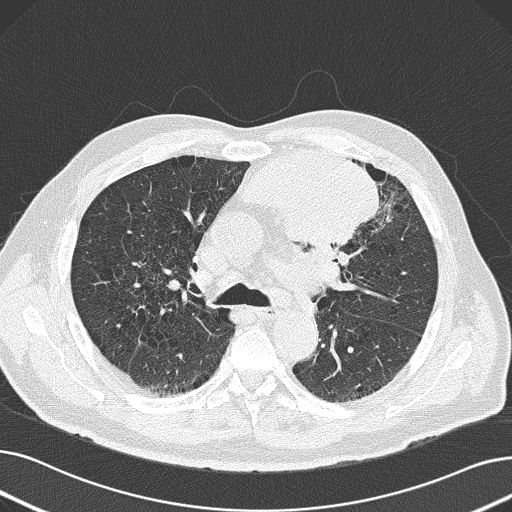
Axial slice from a low-dose chest CT screening exam; baseline annual screen; lung window (W 1500 / L -600 HU); 2 mm slice thickness; lung (sharp) reconstruction kernel (B50f); 120 kVp; slice 67 of 165 in the series. Male, age 69 years at enrolment.
Expert-annotated lung lesion, box from (x=232, y=139) to (x=383, y=252) px. Reader record for this screening exam (exam-level; its link to the box is not recorded): non-calcified nodule or mass ≥4 mm, left upper lobe, 6 × 10 mm, spiculated (stellate) margins, soft tissue attenuation. Official screen result: positive, change unspecified: nodule(s) >= 4 mm or enlarging nodule(s), mass(es), or other non-specific abnormalities suspicious for lung cancer. Lung cancer was diagnosed 20 days after this screen: non-small cell carcinoma, left upper lobe, poorly differentiated (G3), stage IB (AJCC 6th edition), 100 mm at pathology.